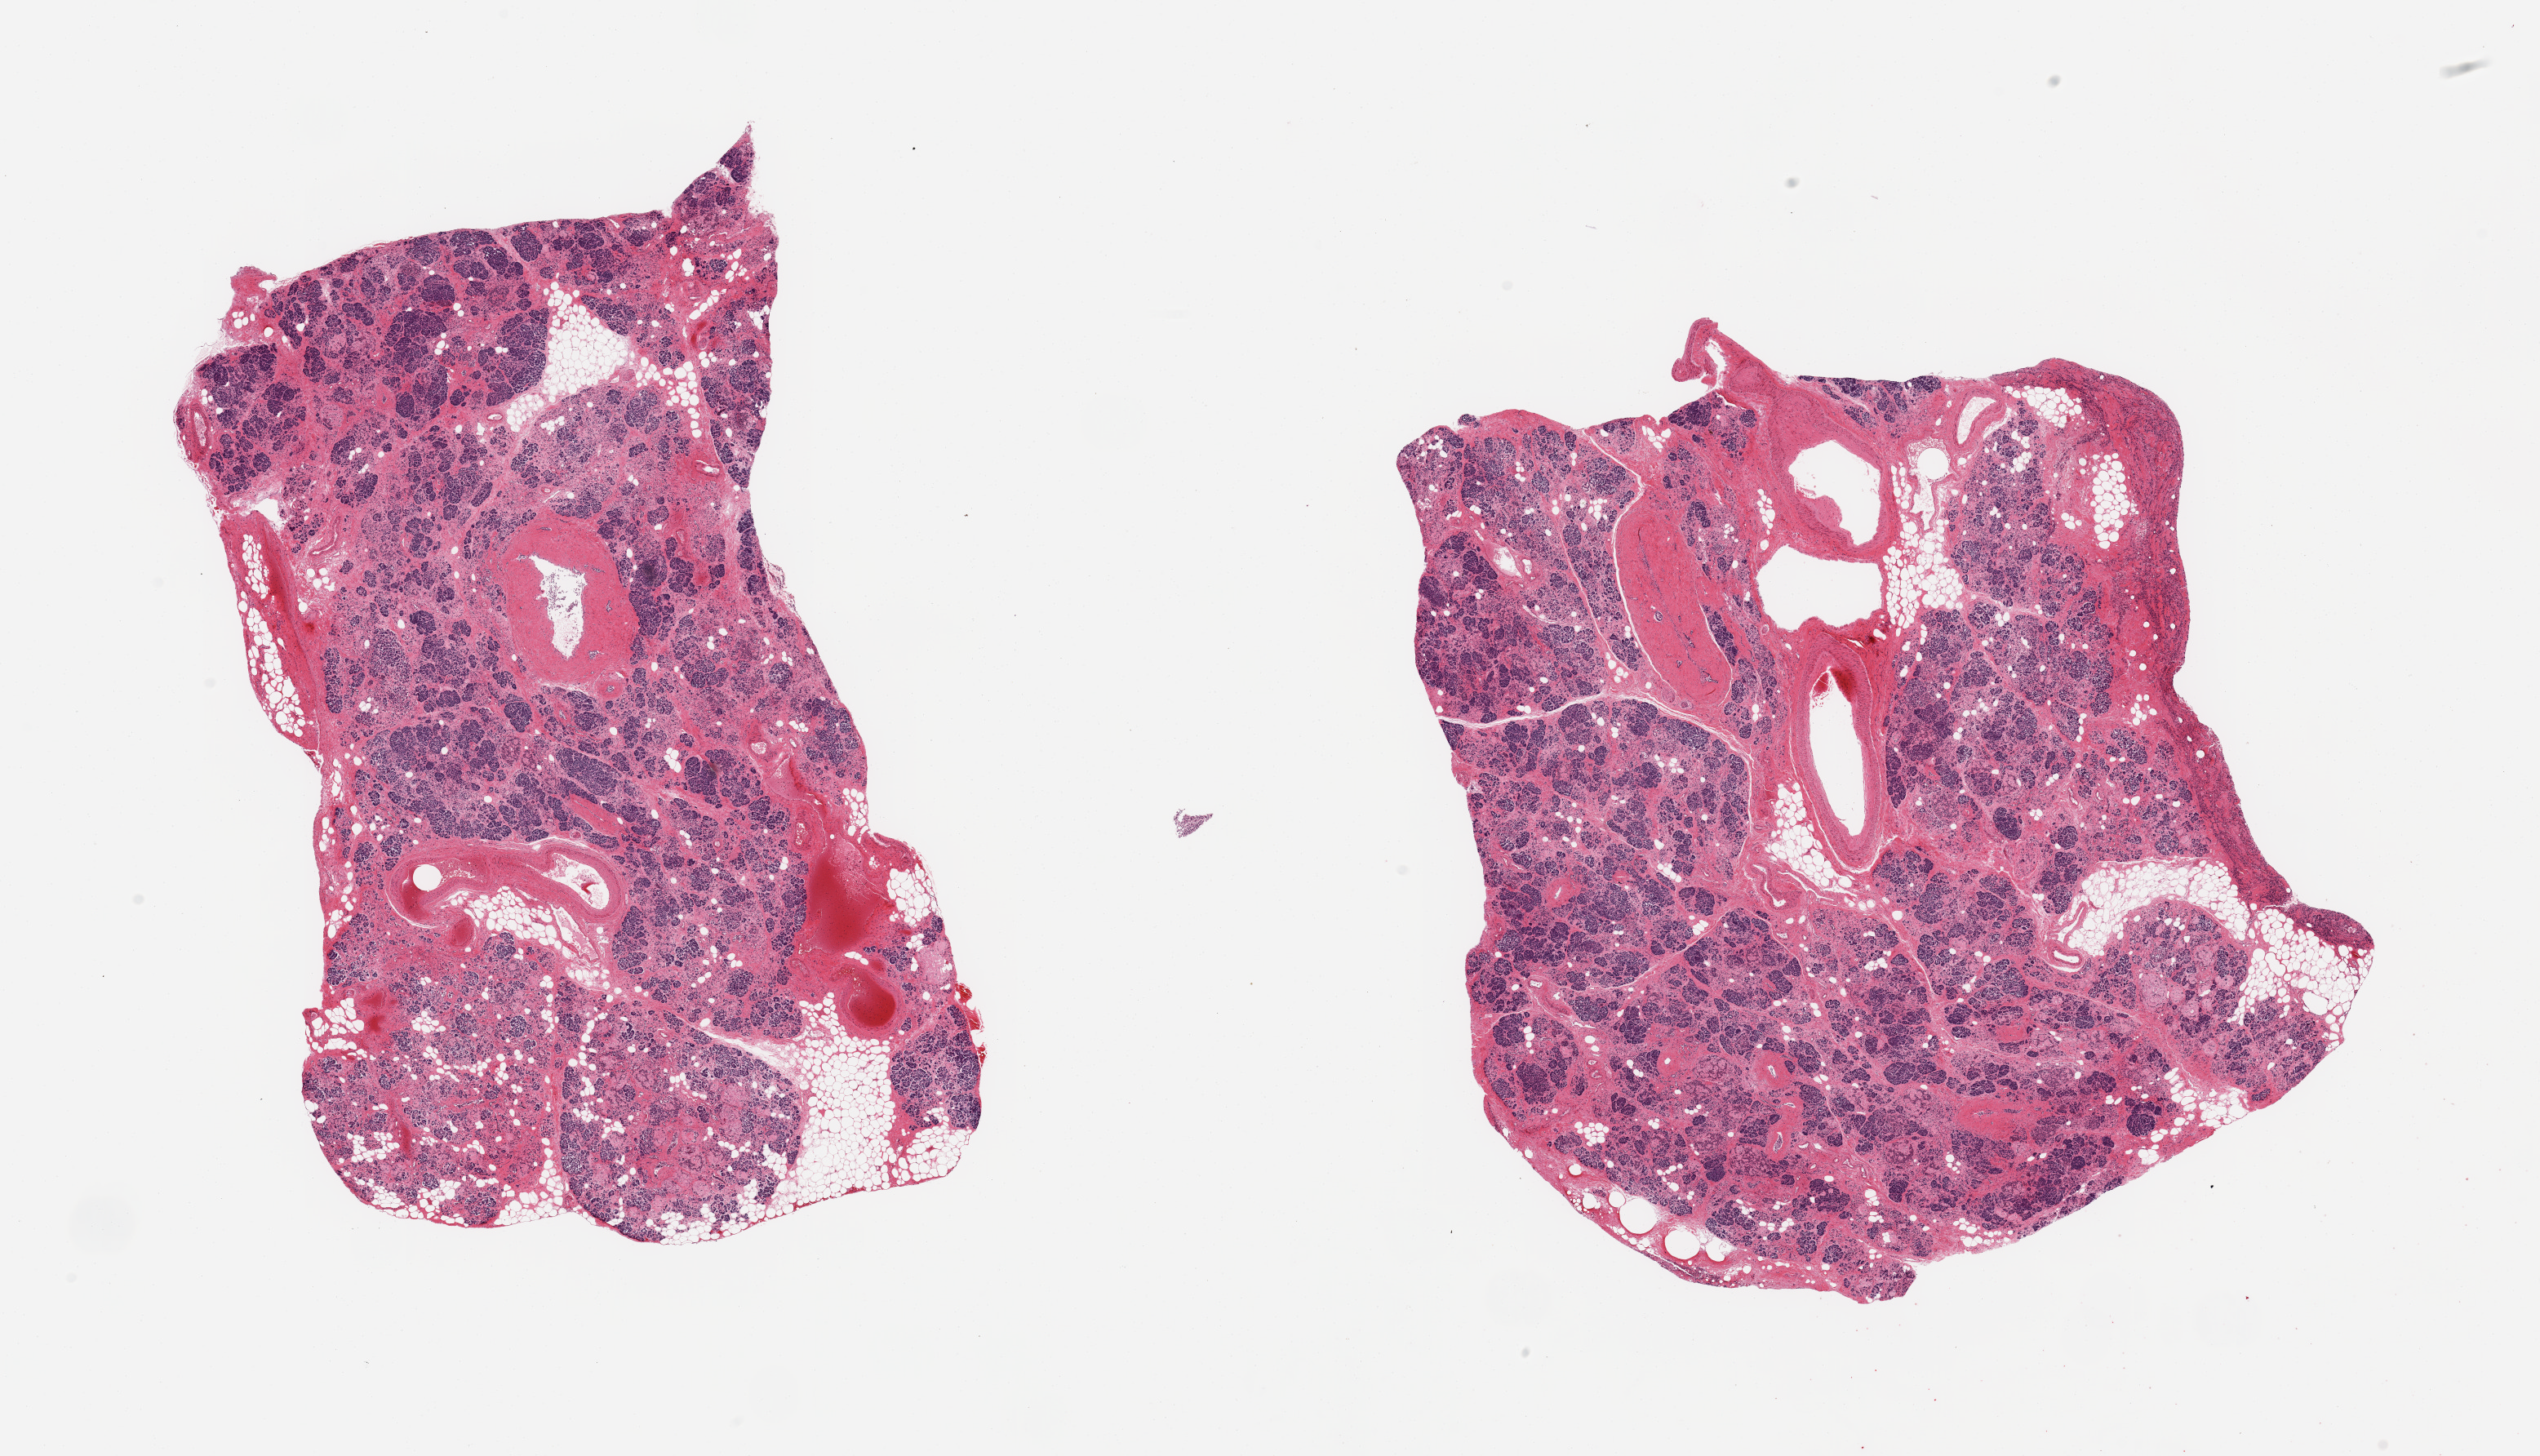
Hematoxylin and eosin (H&E) whole-slide image — whole scanned area (about 24.6 x 14.1 mm, from a 20x scan) shown as a low-resolution overview, PAXgene-fixed paraffin-embedded (PFPE) section, section of pancreas (target tissue), donor tissue sample.
Reviewer comment on this tissue sample: 2 pieces; interacinar and interlobar fibrosis, atrophy, islets with variable replacement by amyloid.